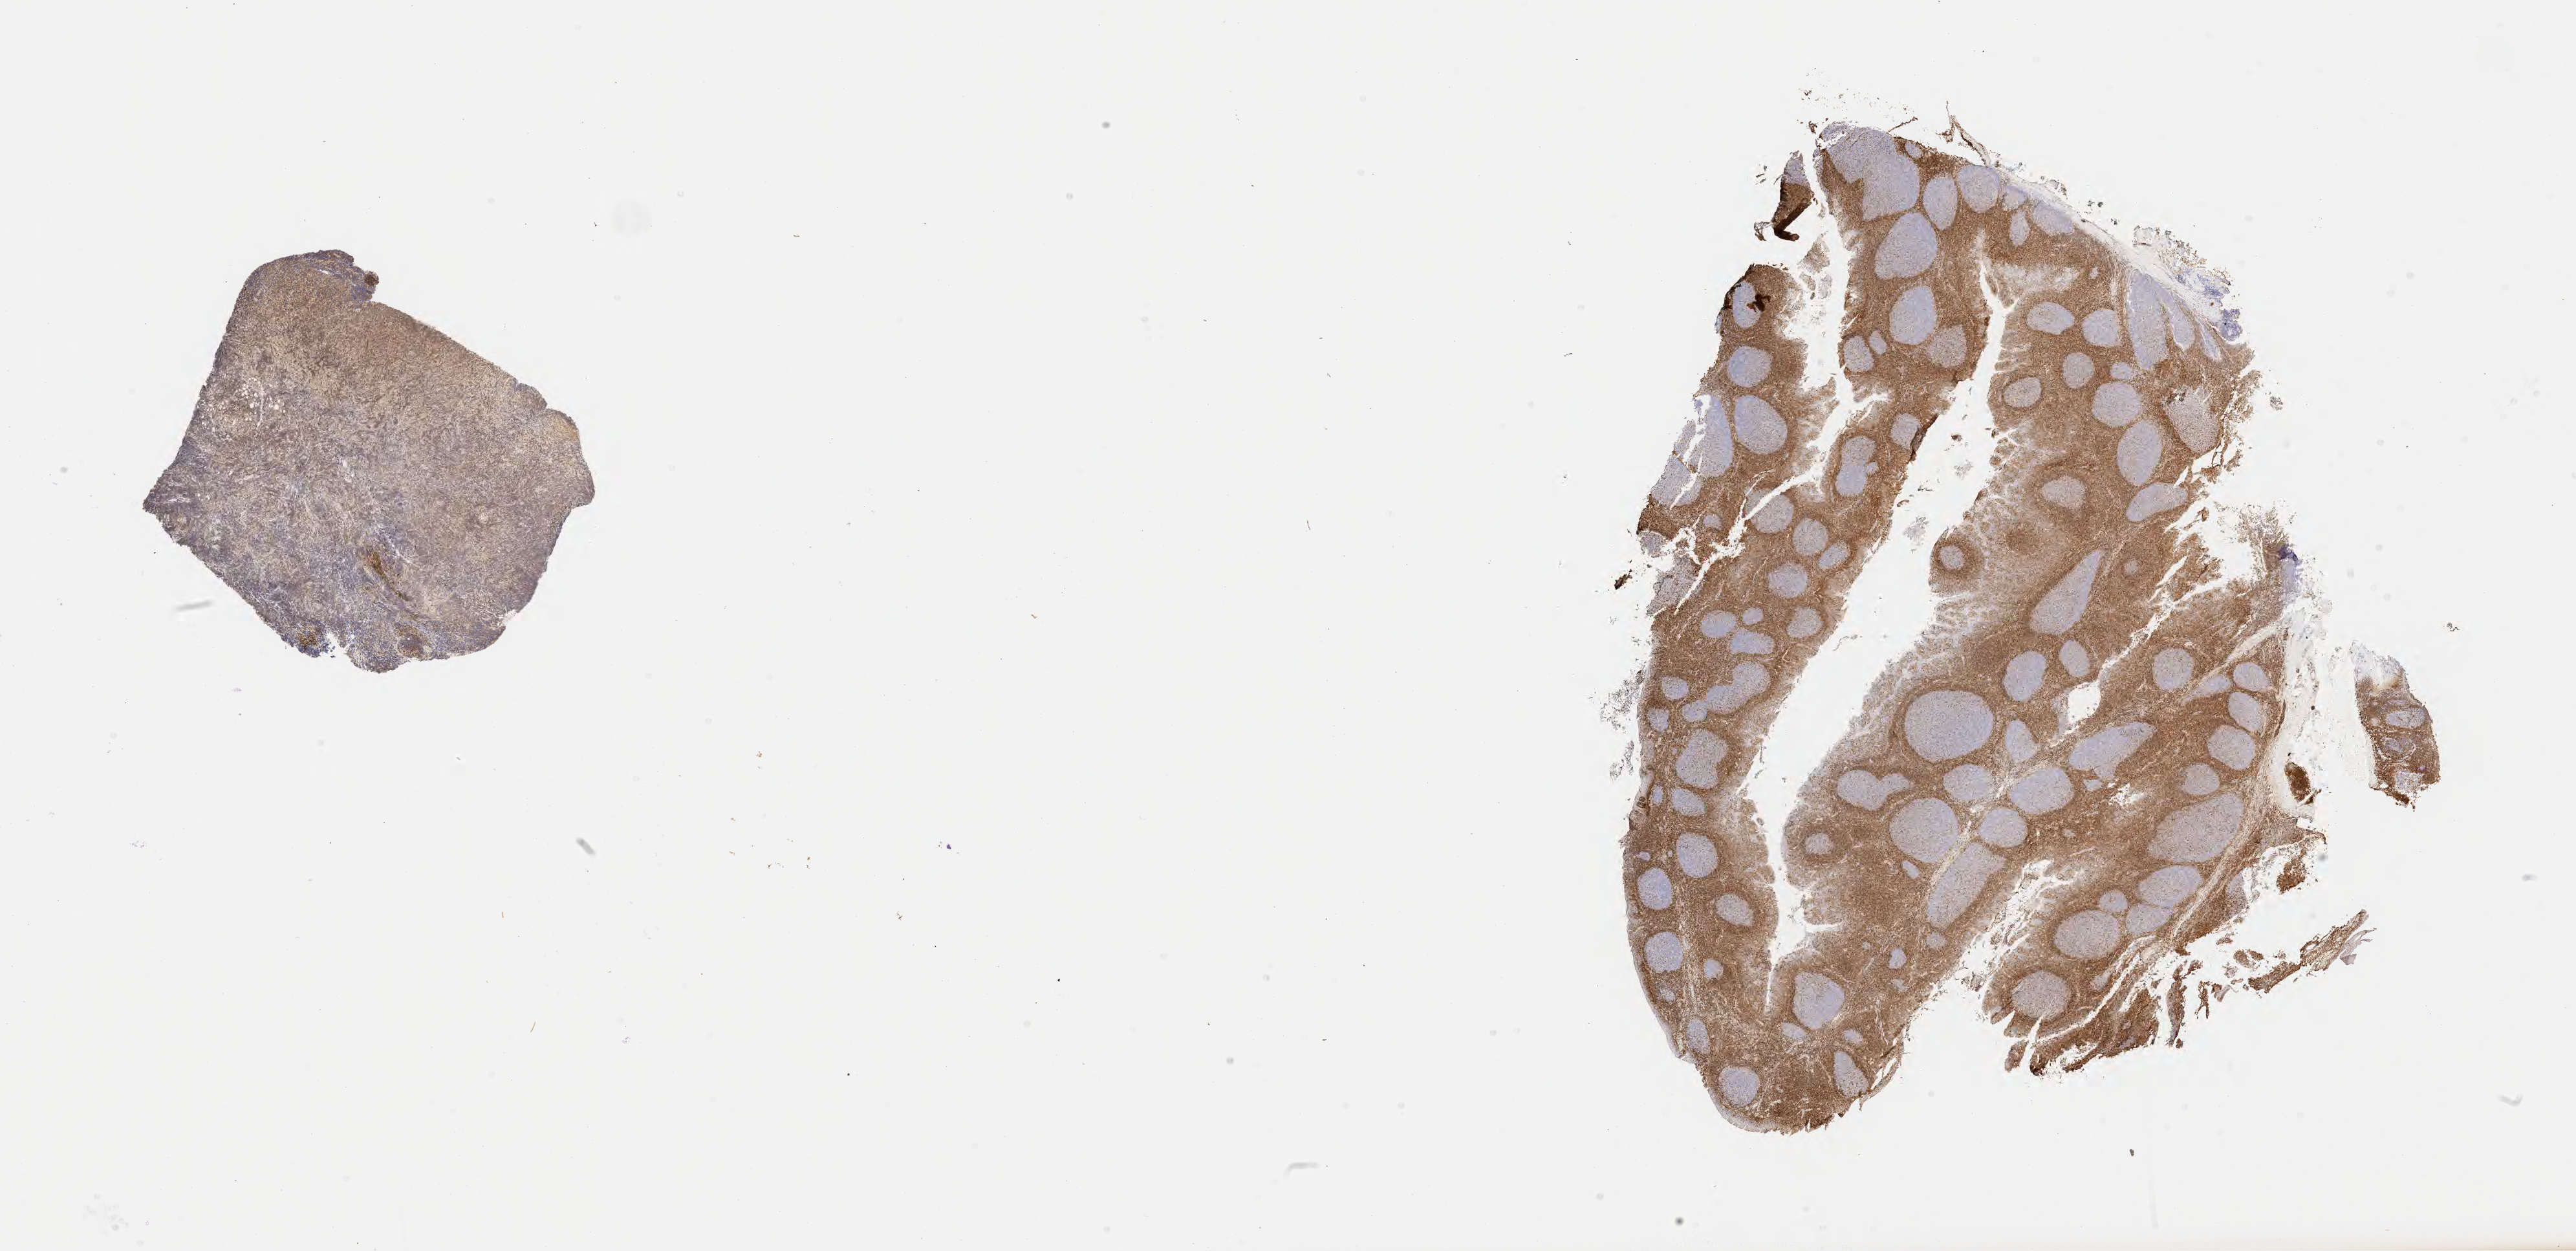
Whole-slide image, immunohistochemical stain for BCL2, low-resolution overview of the scanned area, about 32.2 x 15.6 mm; specimen: tumor tissue; anatomic site: buccal mucosa. Patient: male, age at initial diagnosis 7 years.
Diagnosis: Burkitt lymphoma, NOS.